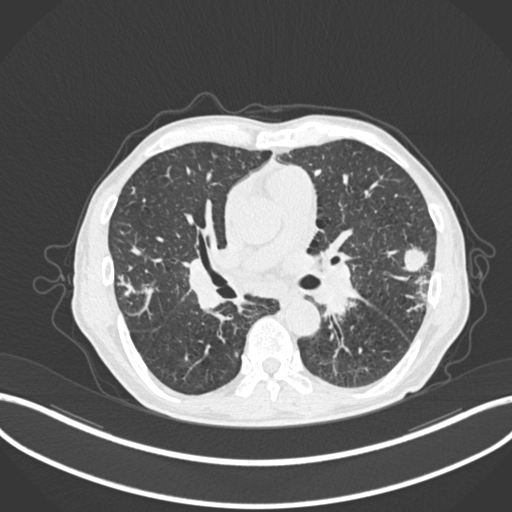
Chest CT, one axial slice. Reconstruction kernel B30f. 120 kVp. Lung window (W 1500 / L -600 HU). 1 mm slice thickness. 512 × 512 image matrix, field of view 400 × 400 mm. Patient: male, 74 years. Case-level facts recorded for this patient, not image findings: clinical TNM (as recorded): T2a N1 M0.
Annotated regions visible in this slice (bounding box drawn by a radiologist):
- lung tumour (recorded histology: adenocarcinoma): bounding box <399,242,433,275> (left, top, right, bottom; pixels)